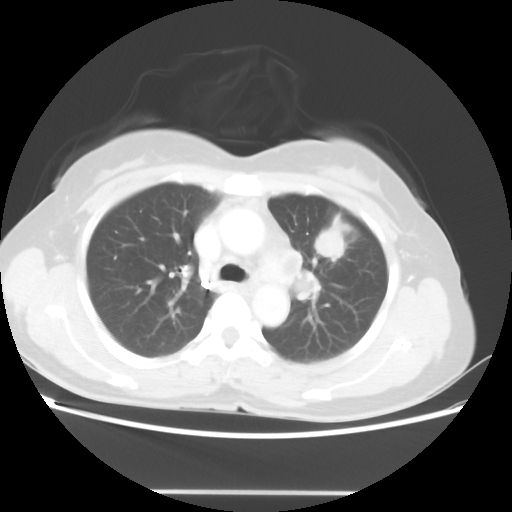
Chest CT, one axial slice. Position 32 of 46 along the scan axis. Reconstruction kernel STANDARD. 100 kVp. Lung window (W 1500 / L -600 HU). 5 mm slice thickness. 512 × 512 image matrix. Patient: female, 50 years. Case-level facts recorded for this patient, not image findings: clinical TNM (as recorded): T1c N1 M0; histopathological grade: G3.
Outlined on this slice (rectangle marked by the reading radiologist):
- lung tumour (recorded histology: adenocarcinoma): box from (x=315, y=218) to (x=345, y=261) px